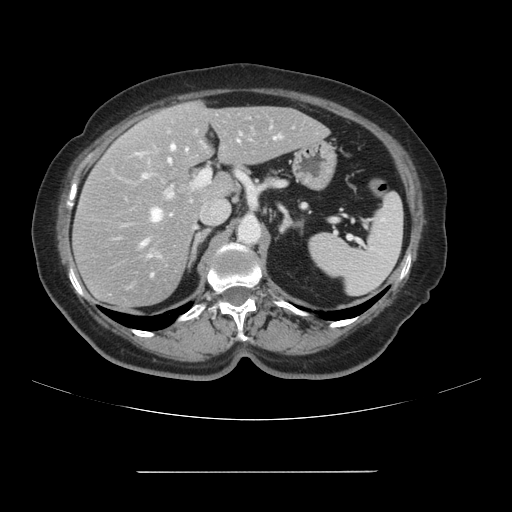
Contrast-enhanced abdominal CT, one axial slice. Position 61 of 111 along the scan axis. Intravenous contrast given. Soft-tissue window (W 400 / L 40 HU). 512 × 512 image matrix. Female patient, age 74 years. From the clinical record (not read from this slice): diagnosis: colorectal cancer liver metastases, imaged before liver resection; multiple liver metastases: yes.
Outlined on this slice (expert manual segmentation):
- hepatic veins: bounding box (x1, y1, x2, y2) in pixels: (142, 136, 278, 256)
- liver: (74, 102, 327, 309)
- planned liver remnant (the part of the liver to remain after resection): (146, 102, 327, 198)
- portal vein (with intrahepatic branches): (141, 120, 319, 199)